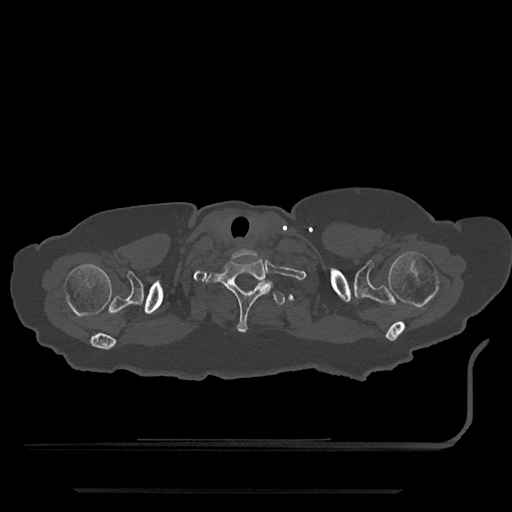
CT including the spine, one axial slice. Reconstruction kernel Br40s/3. Bone window (W 1800 / L 400 HU). 0.5 mm slice thickness. 512 × 512 image matrix. Patient: female, 51 years. From the clinical record (not read from this slice): primary cancer: neuro; vertebrae with lytic lesions (as recorded): T8.
Outlined on this slice (semi-automatically segmented with operator editing):
- T1 vertebra: box from (x=205, y=259) to (x=273, y=333) px
- T2 vertebra: (x=256, y=281)–(x=285, y=306)